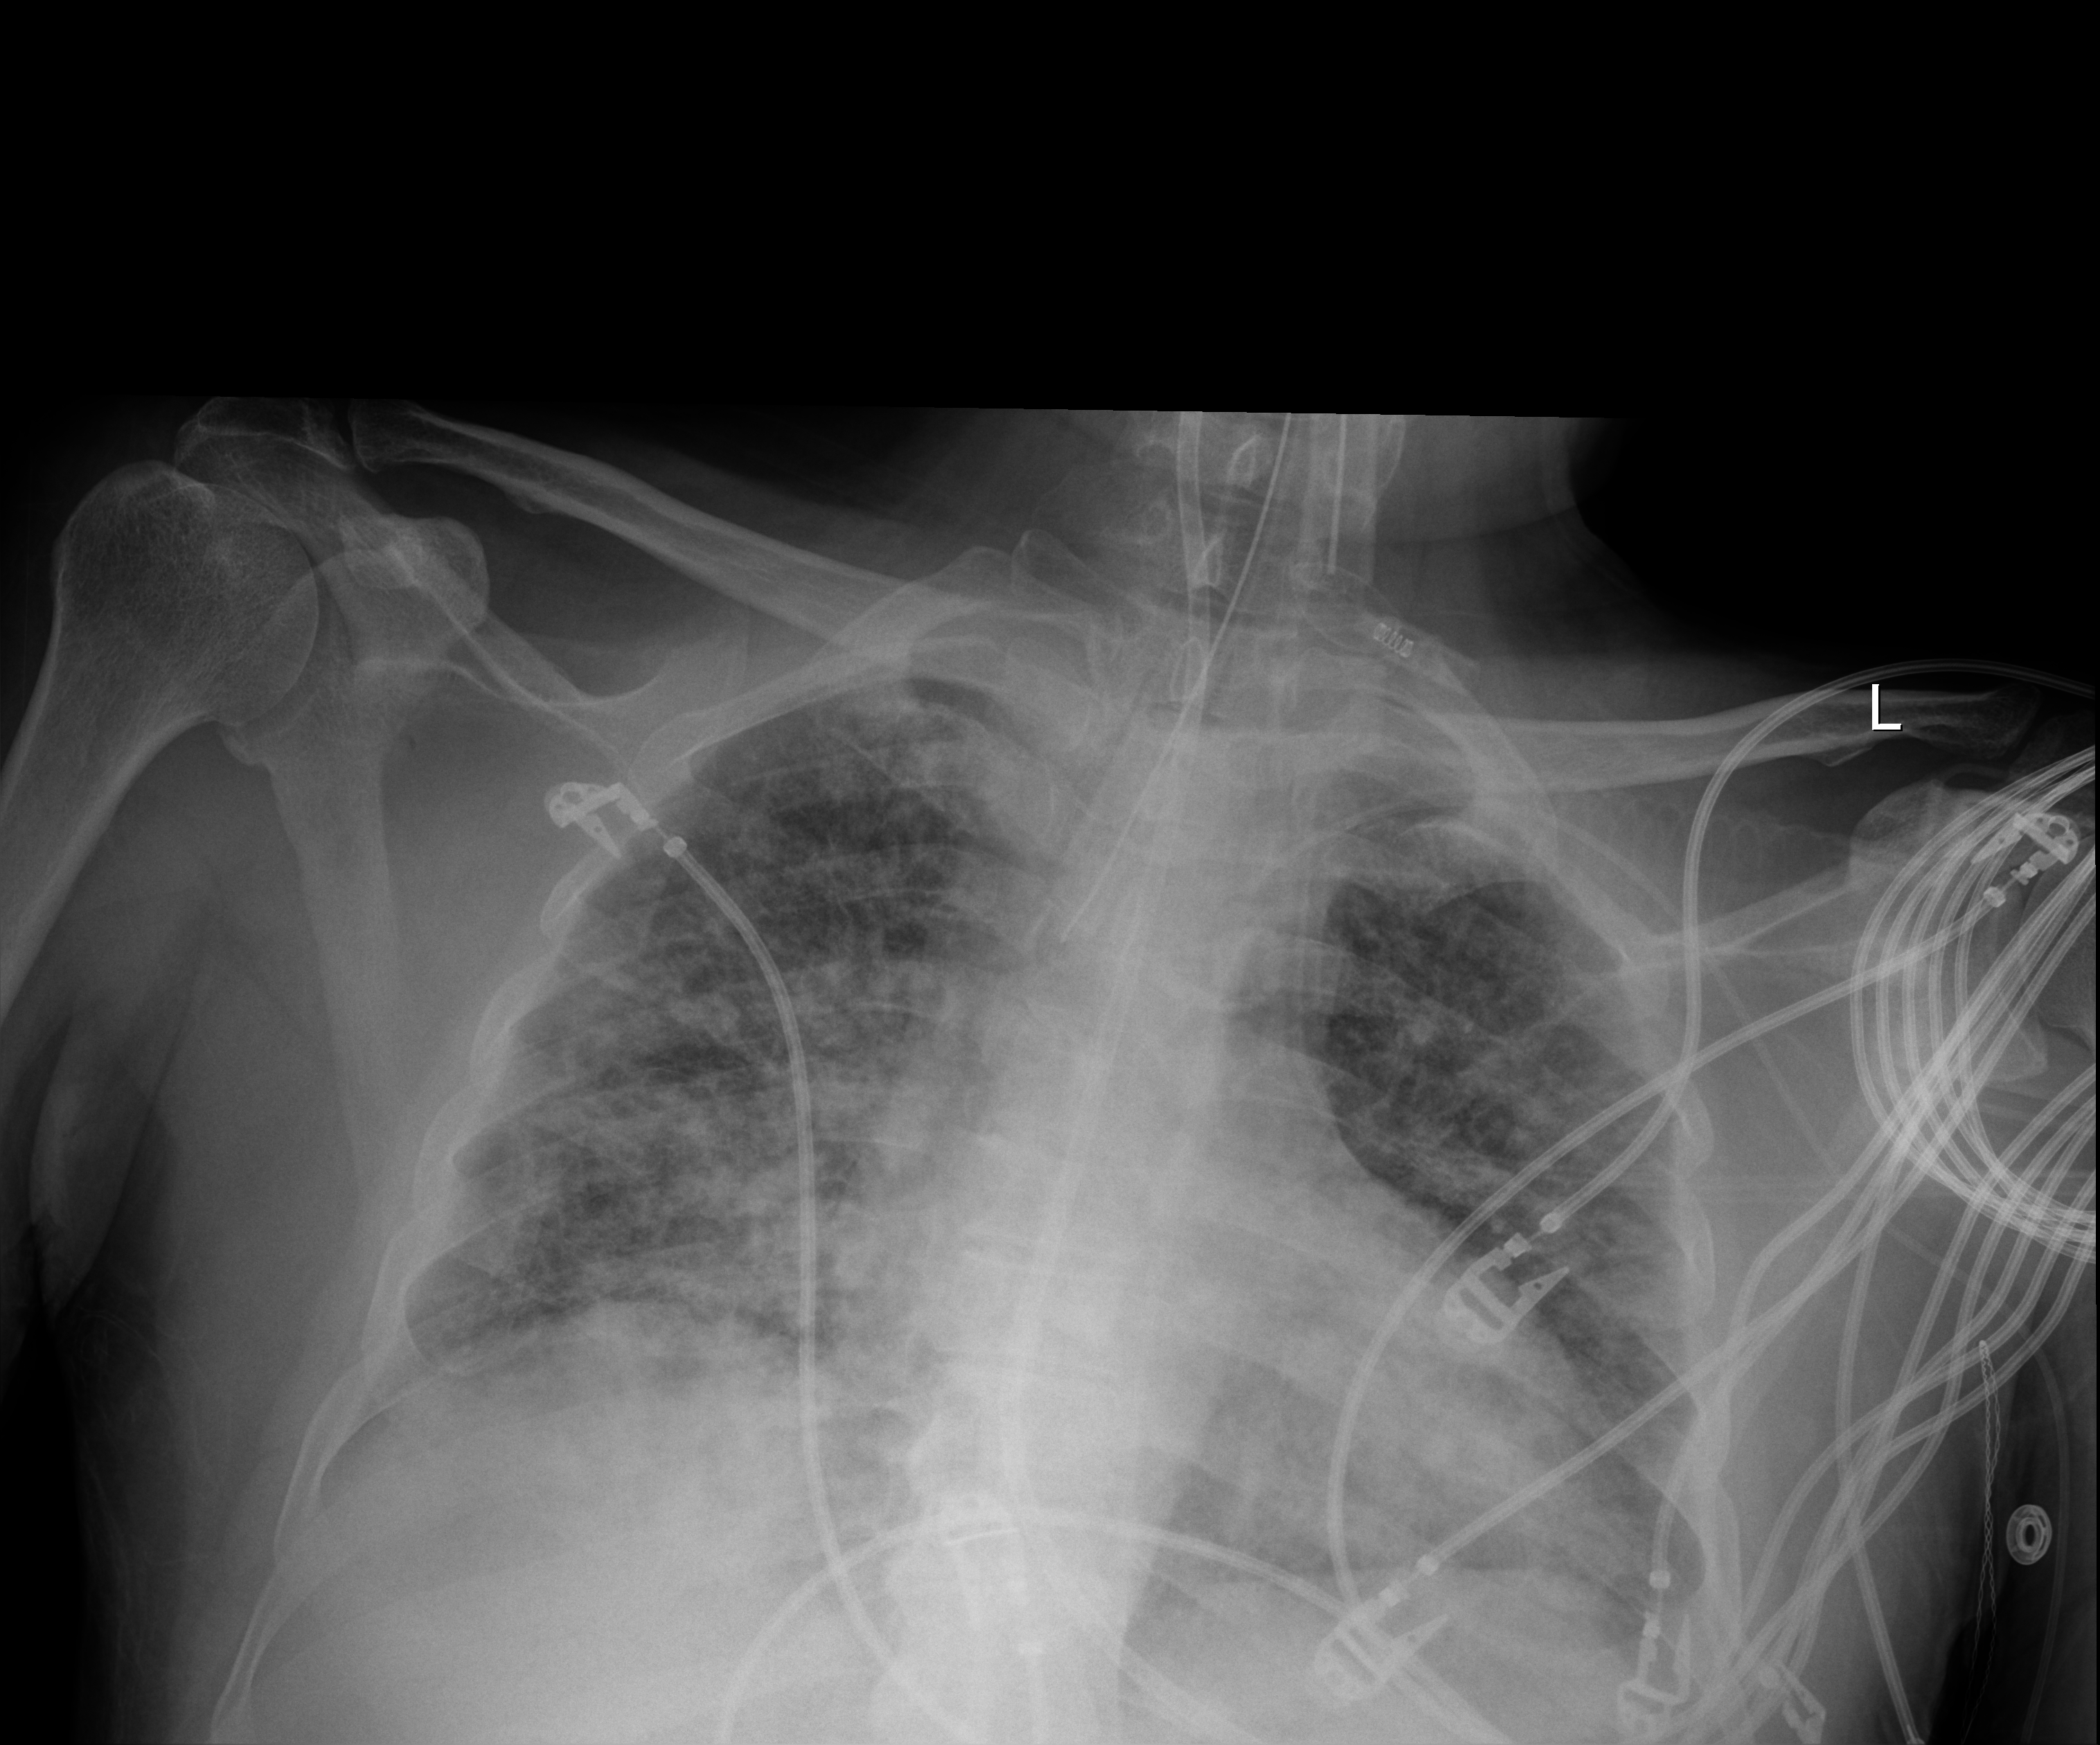
Bedside chest radiograph (digital radiography), anteroposterior (AP) projection. Patient hospitalised with COVID-19; male, aged 18–59 years.
From the hospital-stay record, not from the radiograph (when in the stay this image was taken is not recorded): other chronic lung disease (admission record): no; length of hospital stay: 32 days.